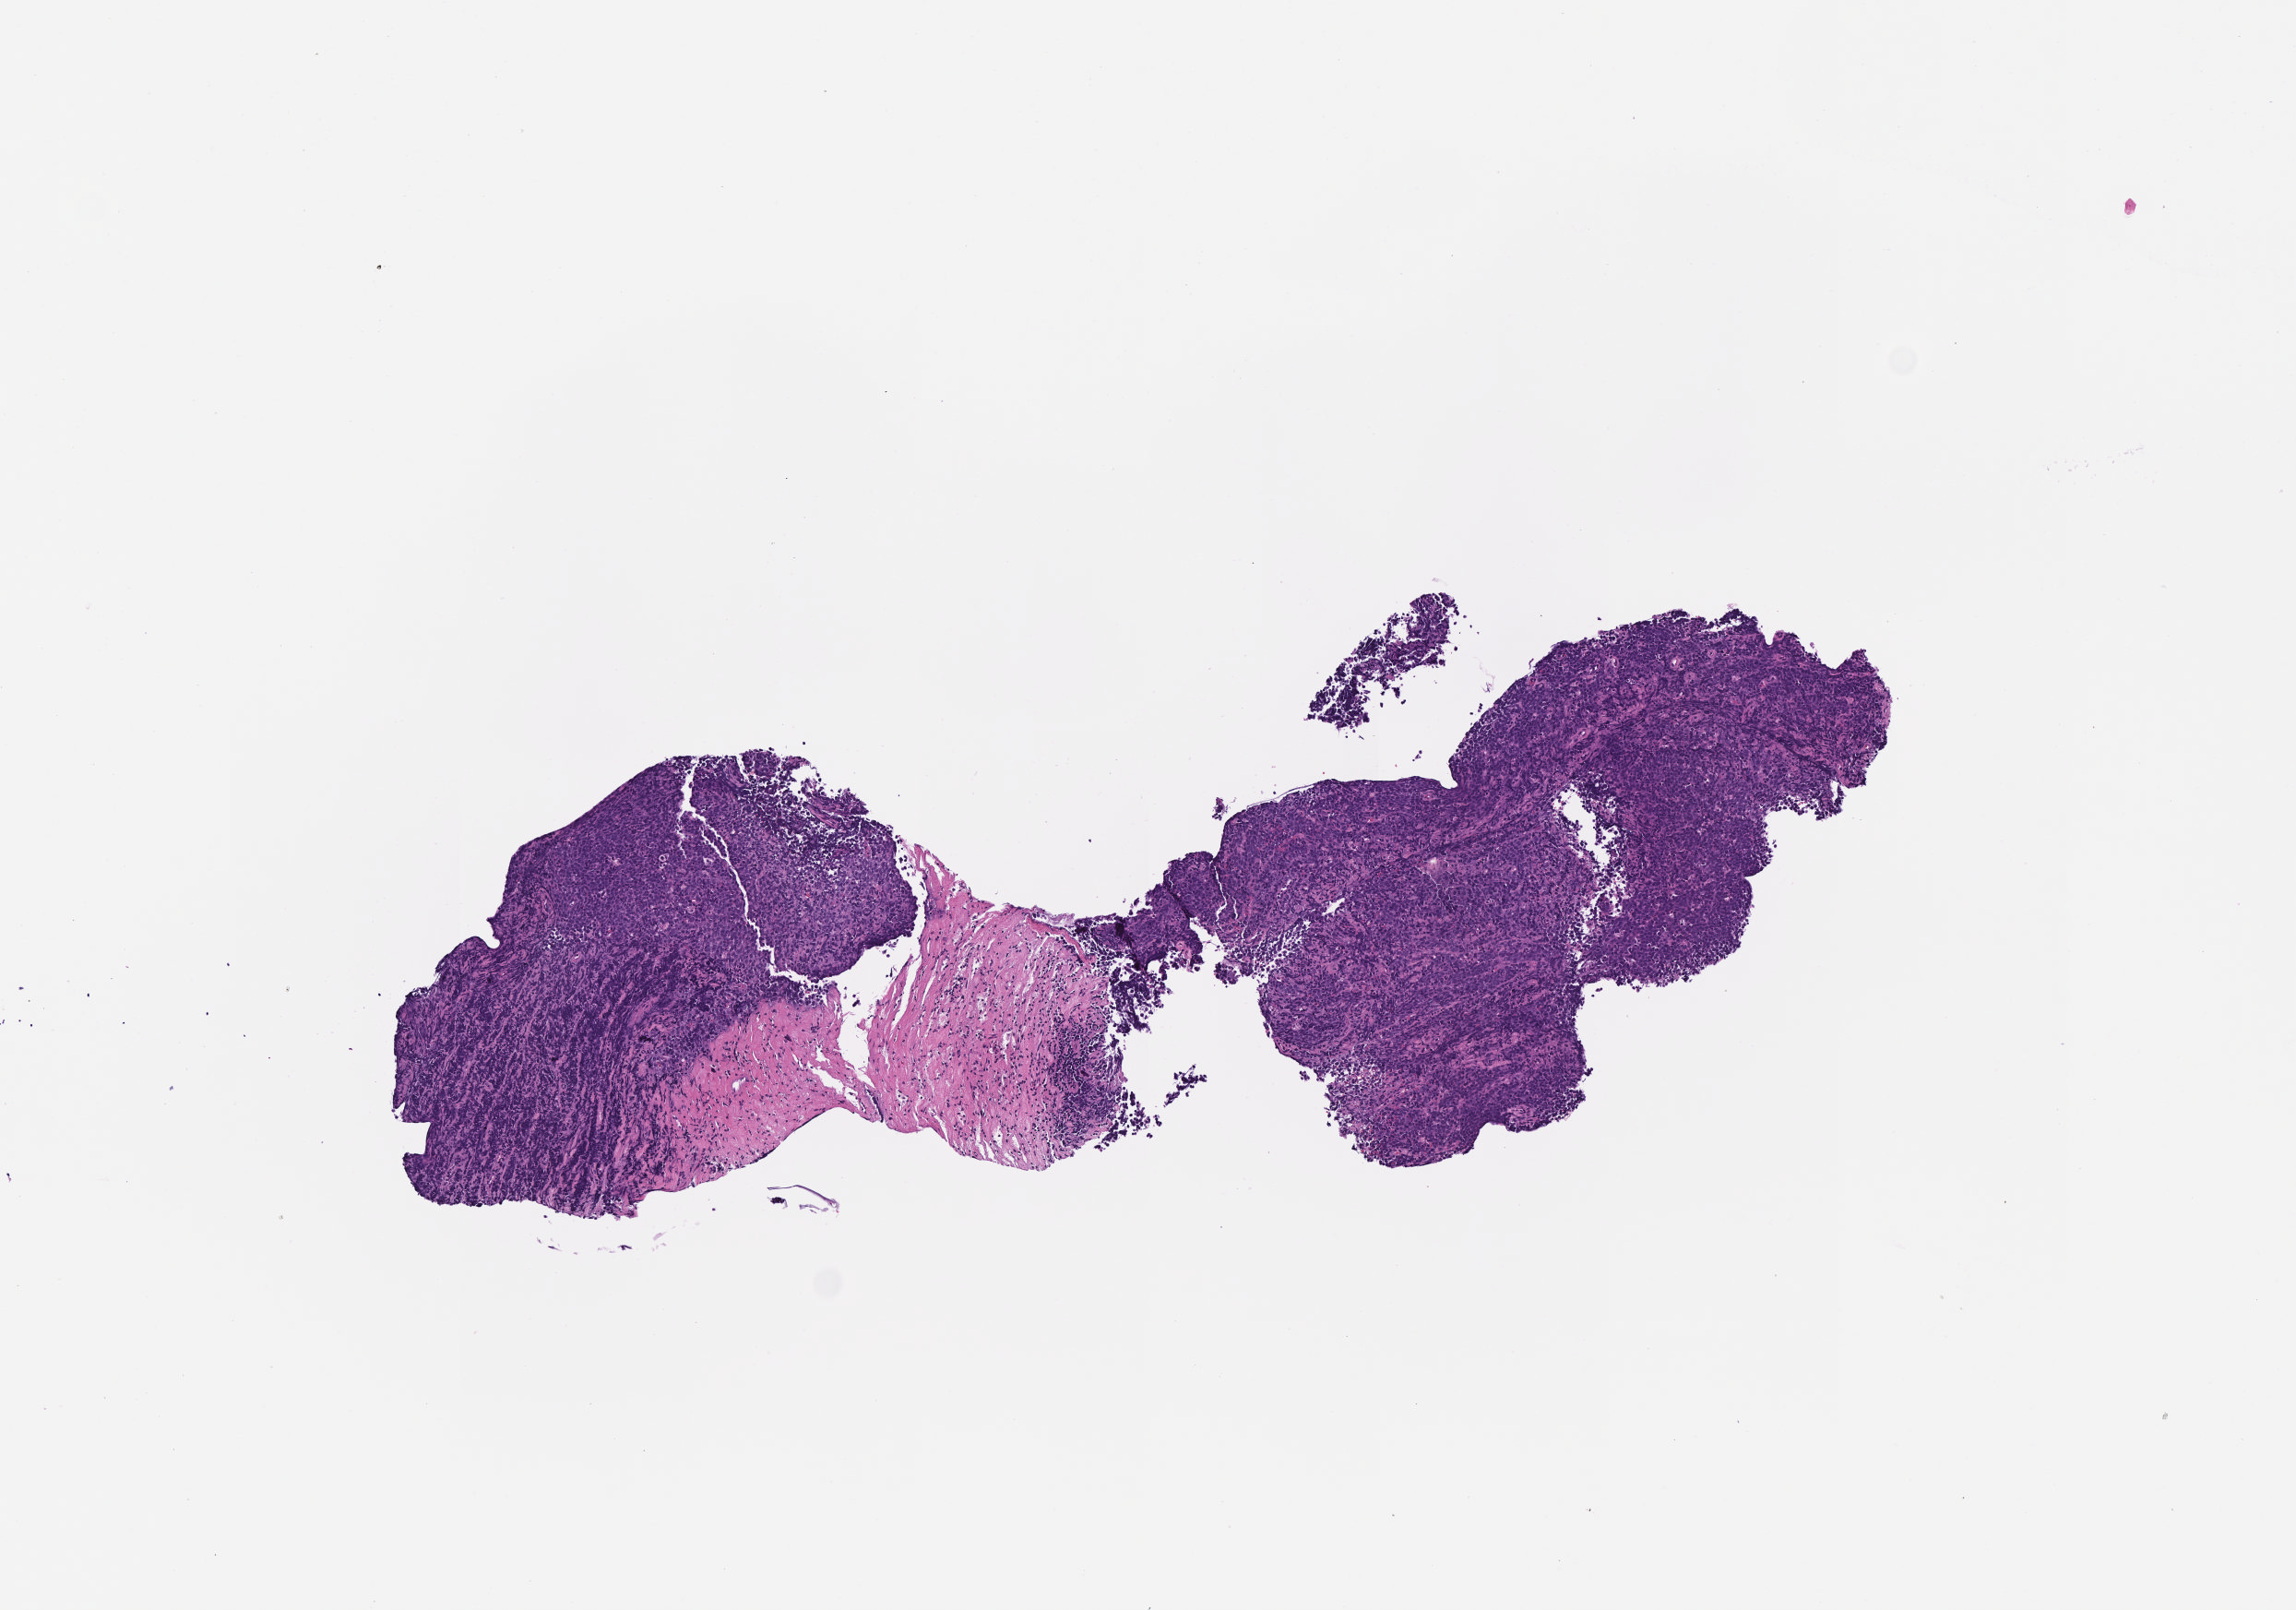
Digitized H&E-stained section — whole scanned area (about 5.0 x 3.5 mm) shown as a low-resolution overview, formalin-fixed, paraffin-embedded (FFPE) tissue, primary tumor. Patient male; age 15 years. Pathologist review of this section (percent, as recorded): tumor cells 90%, tumor nuclei 90%, stromal cells 5%, necrosis 5%, normal cells 0%. Inflammatory infiltration, as recorded: lymphocyte infiltration 20%, monocyte infiltration 30%, neutrophil infiltration 10%.
Ann Arbor stage (patient): Stage IV. Histologic diagnosis: Burkitt lymphoma, NOS. Section: top of the tissue portion.